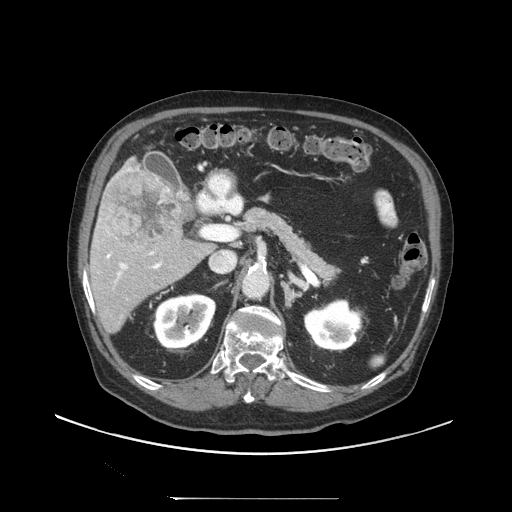
Contrast-enhanced abdominal CT (liver protocol), one axial slice; reconstruction kernel STANDARD; 140 kVp; soft-tissue window (W 400 / L 40 HU); 2.5 mm slice thickness; 512 × 512 image matrix, field of view 450 × 450 mm. Case-level facts recorded for this patient, not image findings: diagnosis: hepatocellular carcinoma (patient treated with transarterial chemoembolisation; whether this scan precedes or follows treatment is not stated here); TNM stage (as recorded): Stage-IIIC; Child-Pugh class: A; tumour differentiation: well differentiated; tumour size: 9.2 cm.
Outlined on this slice (semi-automatic segmentation, software-assisted and operator-edited):
- liver parenchyma outside the tumour (the mass and vessels are separate outlines, so this box may not span the whole liver): box from (x=90, y=158) to (x=210, y=332) px
- mass: (x=103, y=170)–(x=182, y=250)
- liver vessels: (x=99, y=168)–(x=162, y=282)